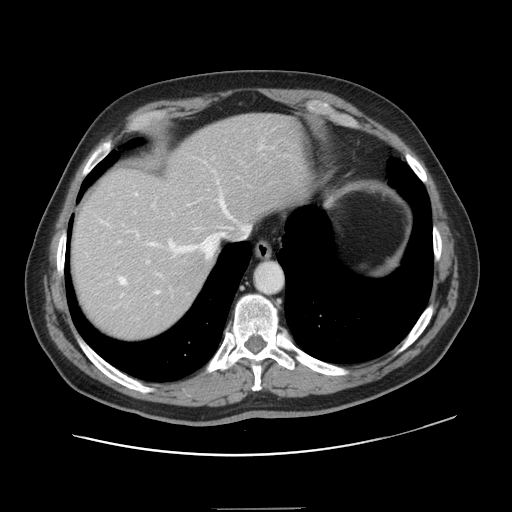
Contrast-enhanced abdominal CT, one axial slice. Position 121 of 143 along the scan axis. 120 kVp. Intravenous contrast given. Soft-tissue window (W 400 / L 40 HU). 2.5 mm slice thickness. 512 × 512 image matrix. Male patient, age 62 years. From the clinical record (not read from this slice): diagnosis: colorectal cancer liver metastases, imaged before liver resection; multiple liver metastases: yes; largest metastasis: 2.7 cm; disease in both lobes: no.
Annotated regions visible in this slice (outlined manually by an expert reader):
- hepatic veins: bounding box (x1, y1, x2, y2) in pixels: (101, 193, 249, 294)
- liver: (73, 114, 305, 339)
- planned liver remnant (the part of the liver to remain after resection): (73, 115, 305, 292)
- portal vein (with intrahepatic branches): (100, 181, 218, 276)